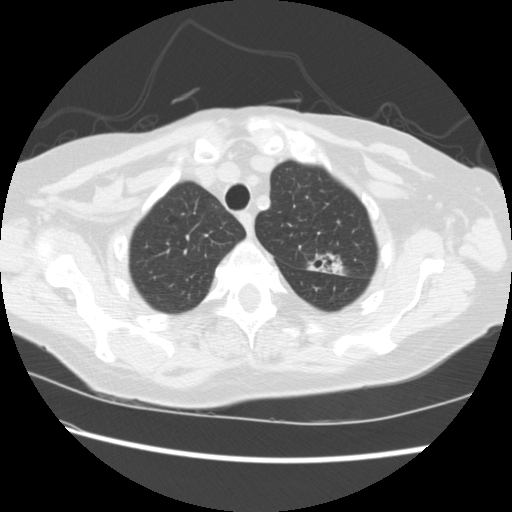
Low-dose screening chest CT, axial slice. Baseline screening round. Lung window (W 1500 / L -600 HU). Standard (soft-tissue) reconstruction kernel (STANDARD). Slice 42 of 224 in the series. Female participant, aged 74 years at enrolment. Former smoker at enrolment.
Lesion marked by an expert reader, bounding box (x1, y1, x2, y2) in pixels: (297, 244, 347, 283). The screening reader recorded 2 non-calcified nodules or masses ≥4 mm on this exam; which of them this box marks is not recorded. Official screen result: positive, change unspecified: nodule(s) >= 4 mm or enlarging nodule(s), mass(es), or other non-specific abnormalities suspicious for lung cancer. Participant outcome: lung cancer diagnosed 309 days after this screen — non-small cell carcinoma, left upper lobe, stage IV (AJCC 6th edition).